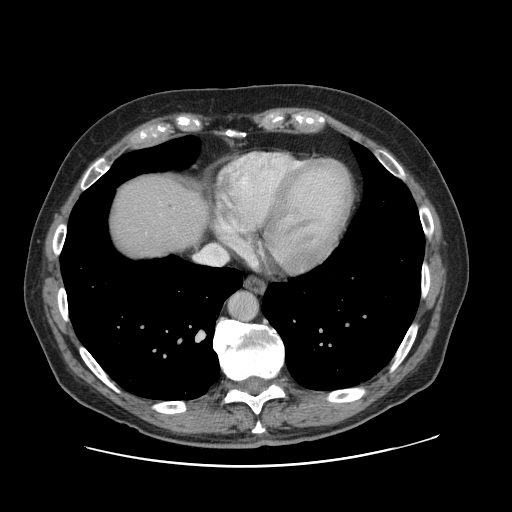
Contrast-enhanced abdominal CT, one axial slice; position 113 of 138 along the scan axis; 120 kVp; intravenous contrast given; soft-tissue window (W 400 / L 40 HU); 2.5 mm slice thickness; 512 × 512 image matrix, field of view 402 × 402 mm. Male patient, age 71 years. From the clinical record (not read from this slice): diagnosis: colorectal cancer liver metastases, imaged before liver resection; multiple liver metastases: no.
Structures marked on this image (expert manual segmentation):
- liver: bounding box (x1, y1, x2, y2) in pixels: (108, 172, 209, 261)
- planned liver remnant (the part of the liver to remain after resection): (108, 174, 206, 262)